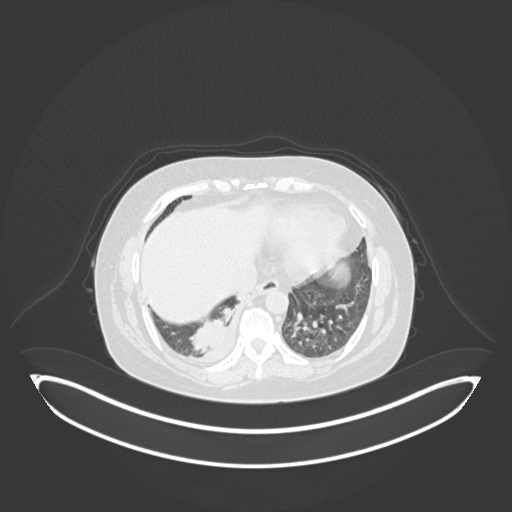
Chest CT, one axial slice. Position 34 of 231 along the scan axis. Reconstruction kernel B30f. 120 kVp. Lung window (W 1500 / L -600 HU). 512 × 512 image matrix, field of view 500 × 500 mm. Patient: female, 56 years. Case-level facts recorded for this patient, not image findings: clinical TNM (as recorded): T2b N1 M0; histopathological grade: G3.
Annotated regions visible in this slice (rectangle marked by the reading radiologist):
- lung tumour (recorded histology: small cell carcinoma): bounding box [x1, y1, x2, y2] px = [189, 300, 236, 361]